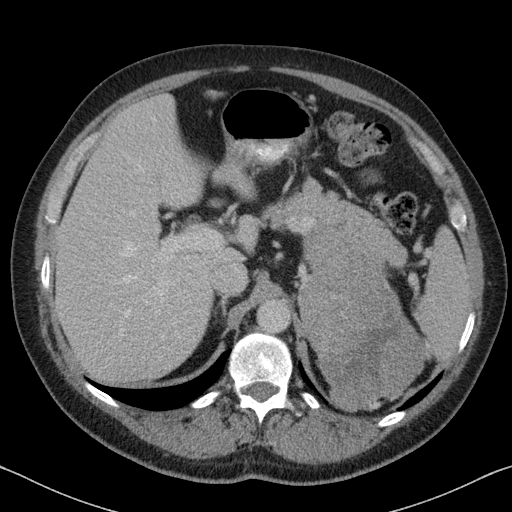
Contrast-enhanced abdominal CT, one axial slice; slice 56 of 88 in the series (ordered by position); 120 kVp; intravenous contrast given; soft-tissue window (W 400 / L 40 HU); 3 mm slice thickness; 512 × 512 image matrix. Patient: male, 51 years. From the clinical record (not read from this slice): diagnosis: adrenocortical carcinoma; tumour side: left adrenal; tumour size at pathology: 16.5 cm; Ki-67 index: 30 %; stage (as recorded): 2.
Structures marked on this image (semi-automatically segmented with operator editing):
- mass: bounding box (x1, y1, x2, y2) in pixels: (304, 231, 422, 406)